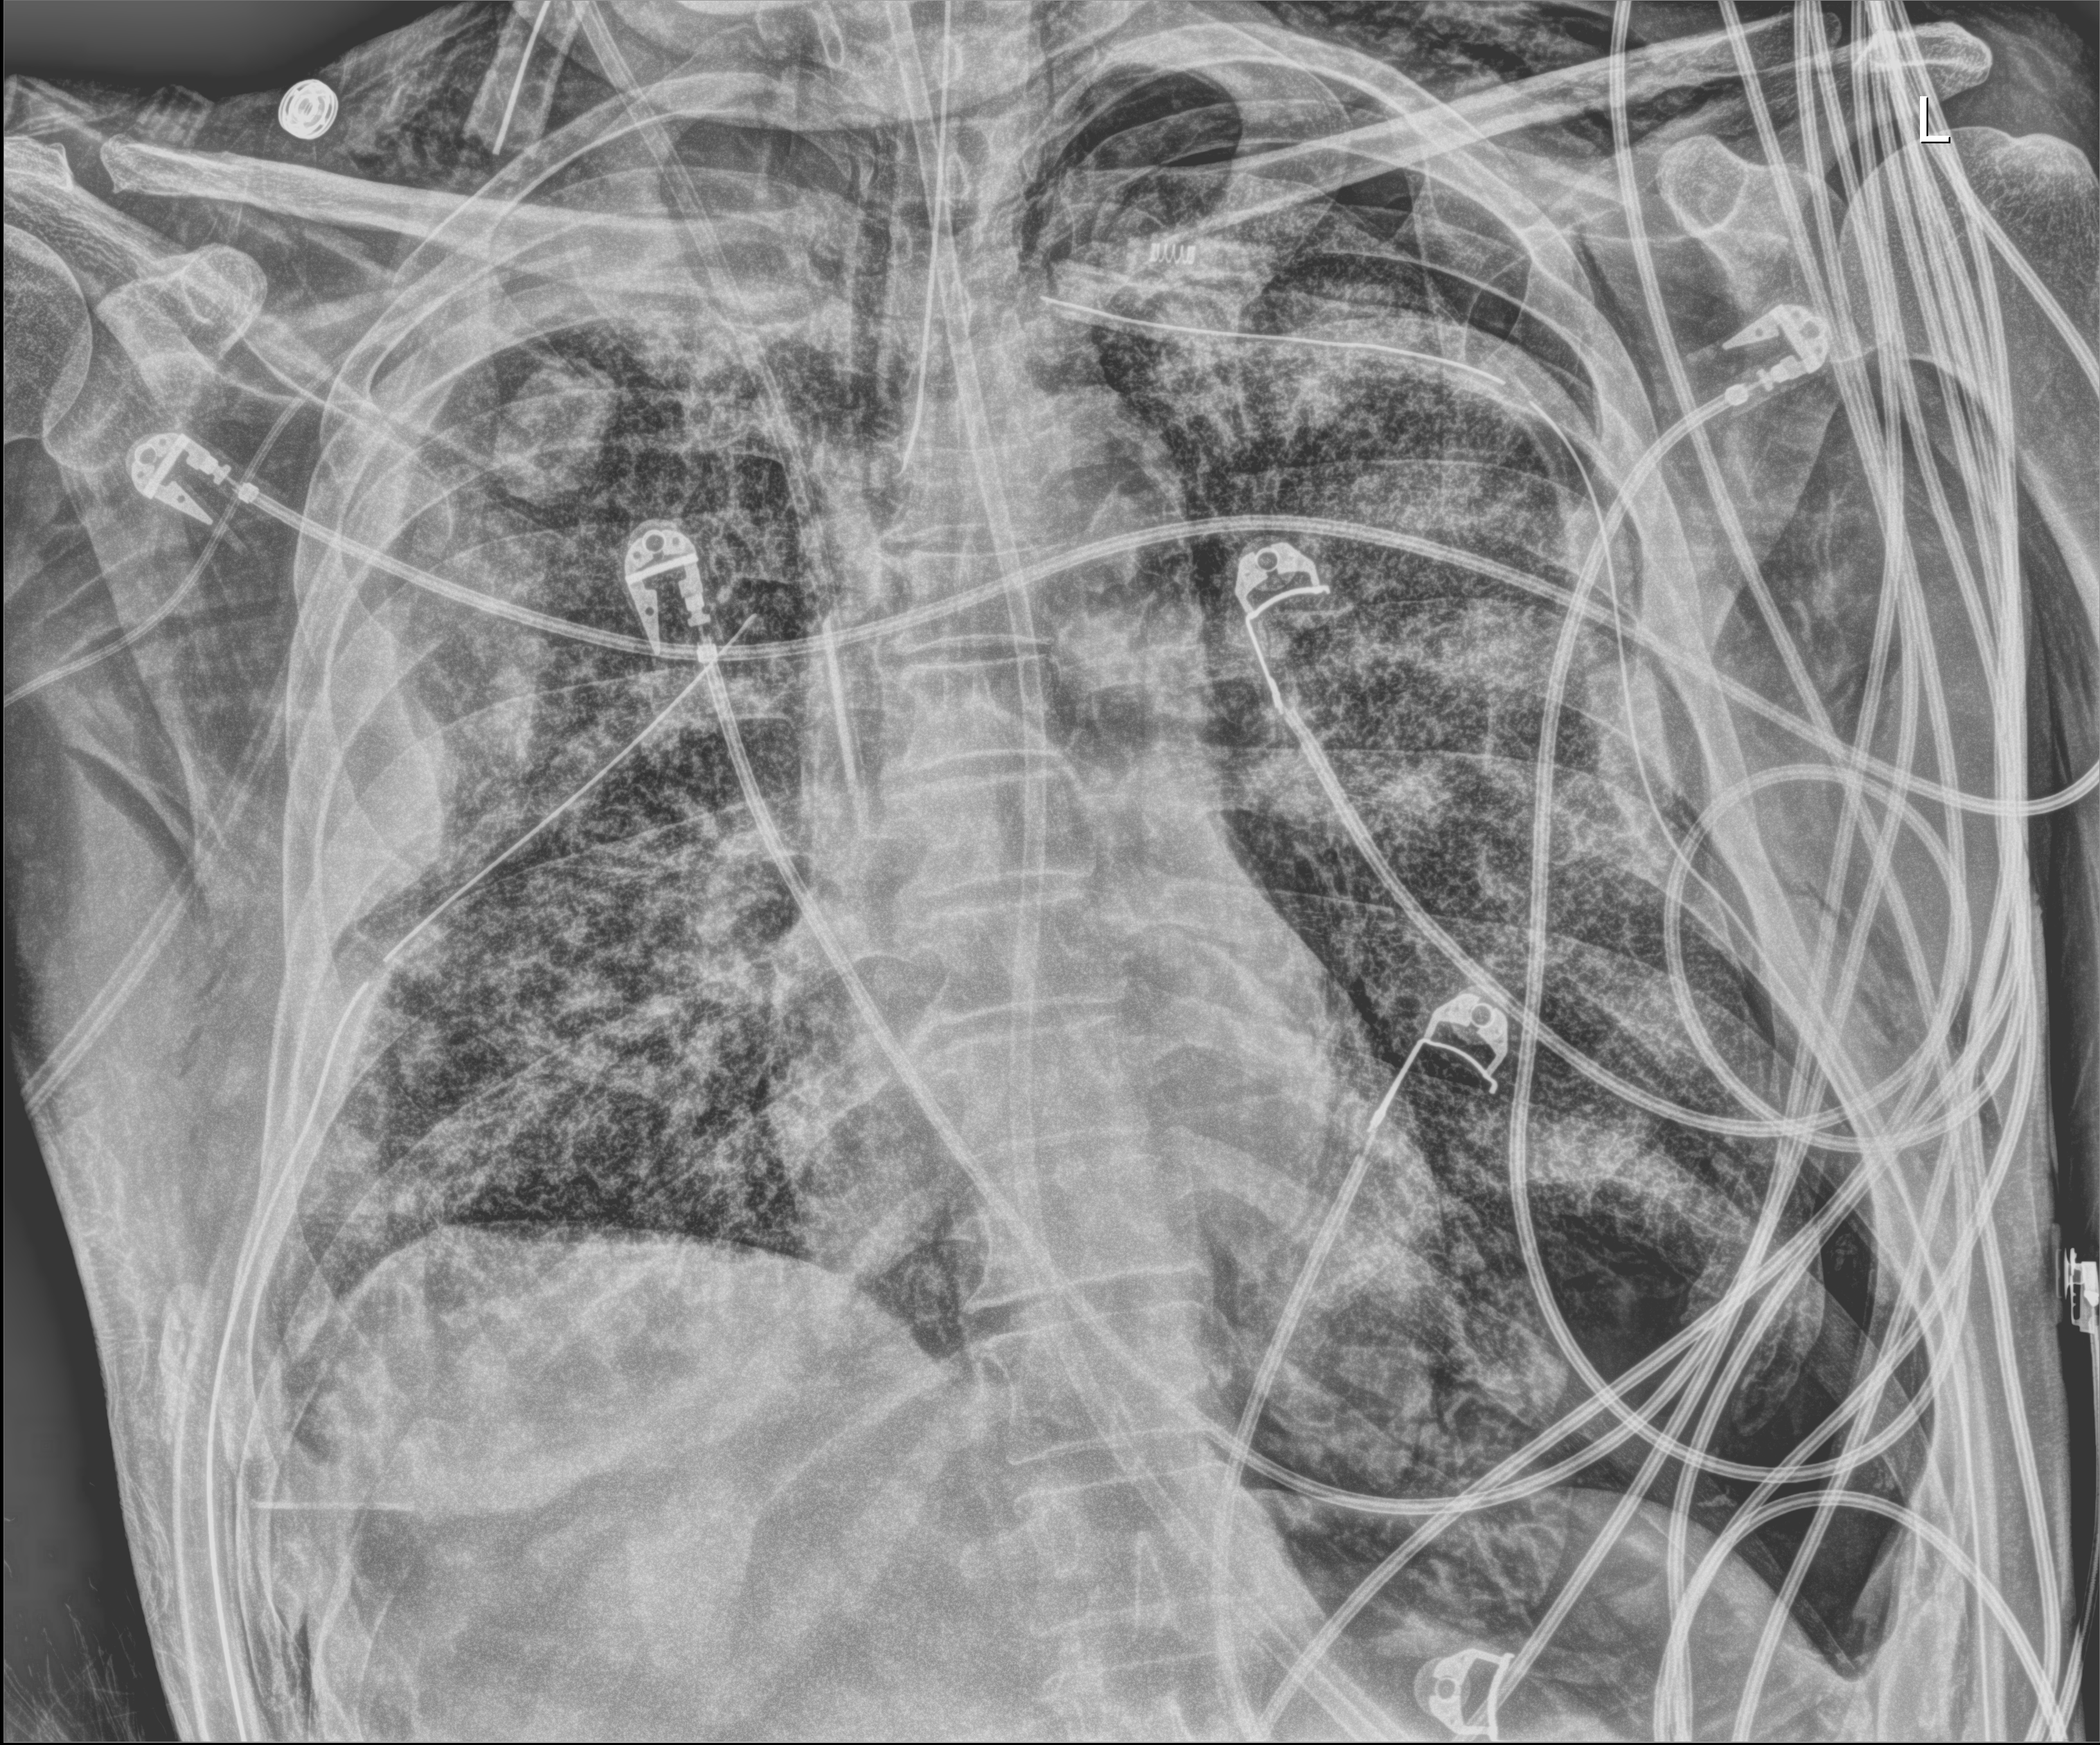
Chest radiograph; anteroposterior (AP) projection. Male patient hospitalised with COVID-19, age 18–59 years.
From the hospital-stay record, not from the radiograph (when in the stay this image was taken is not recorded): admitted to intensive care during this hospital stay: yes.